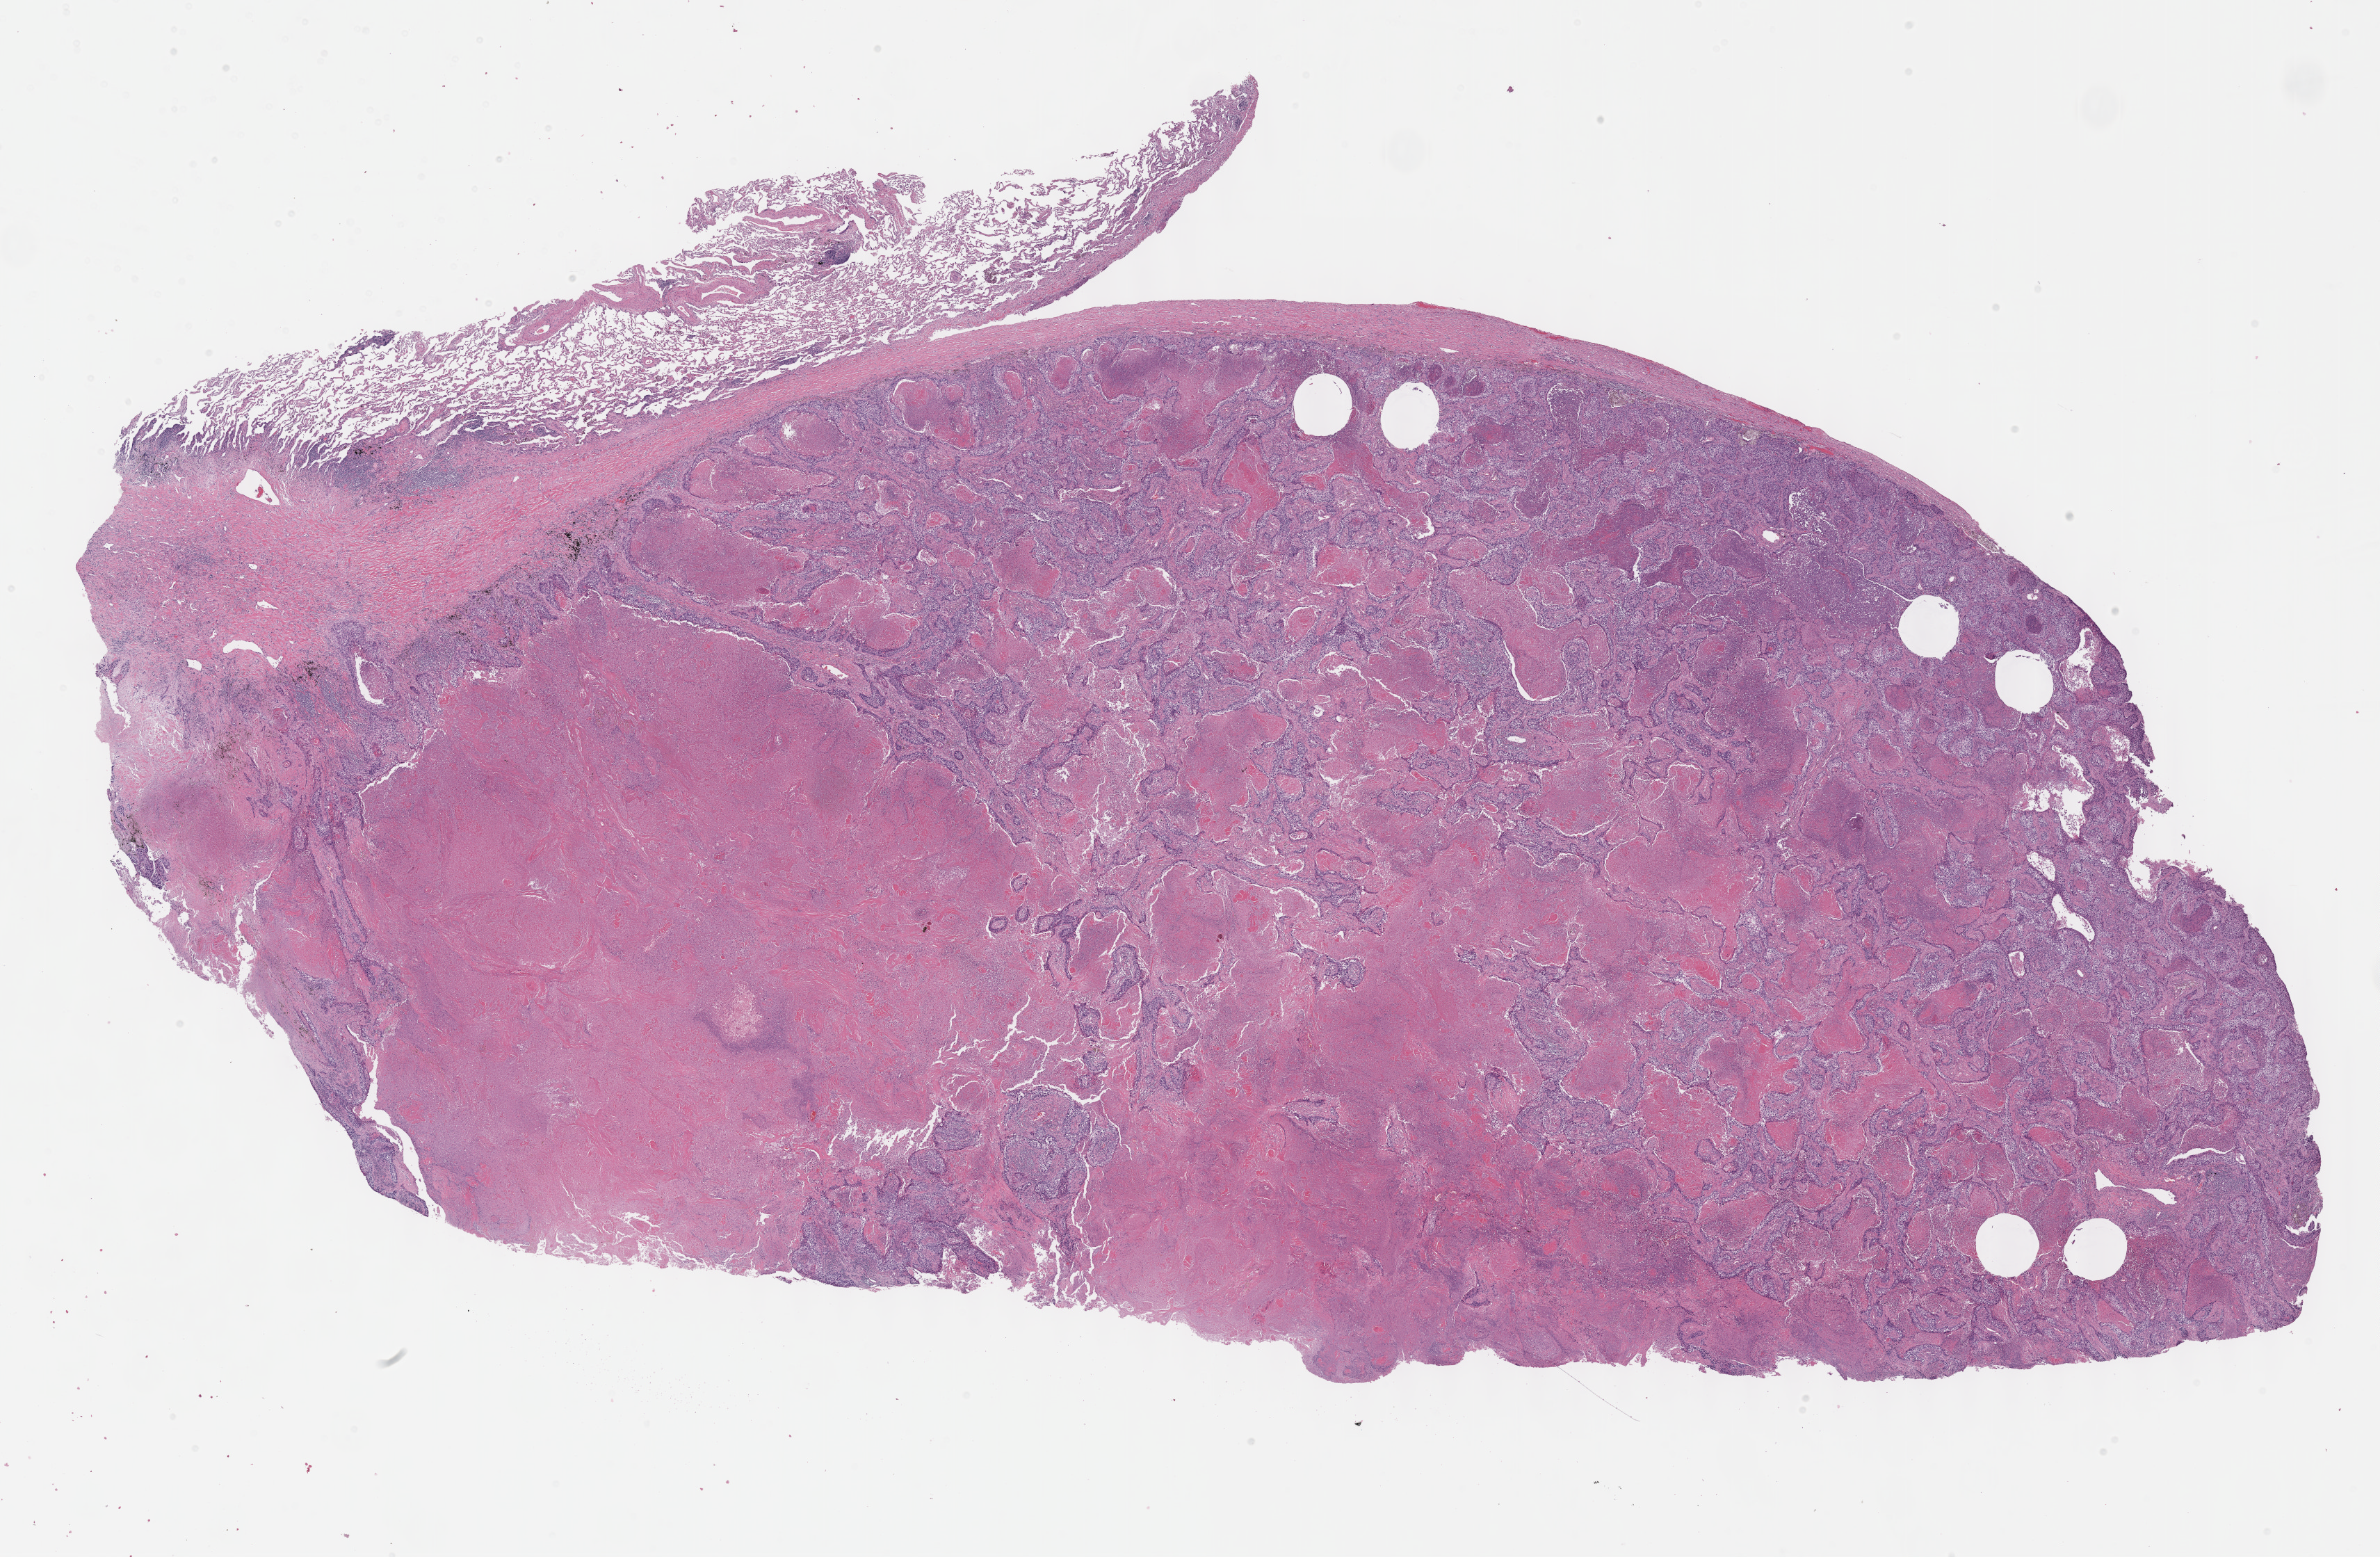
Hematoxylin and eosin (H&E) stained whole-slide image, whole scanned area (about 27.7 x 18.1 mm) shown as a low-resolution overview. Formalin-fixed paraffin-embedded (FFPE) diagnostic section. Sample: primary tumour, lung. Patient: male, age at initial diagnosis 77 years.
• AJCC pathologic stage: IIA (7th edition)
• pathologic diagnosis: Squamous cell carcinoma, NOS (lower lobe, lung)